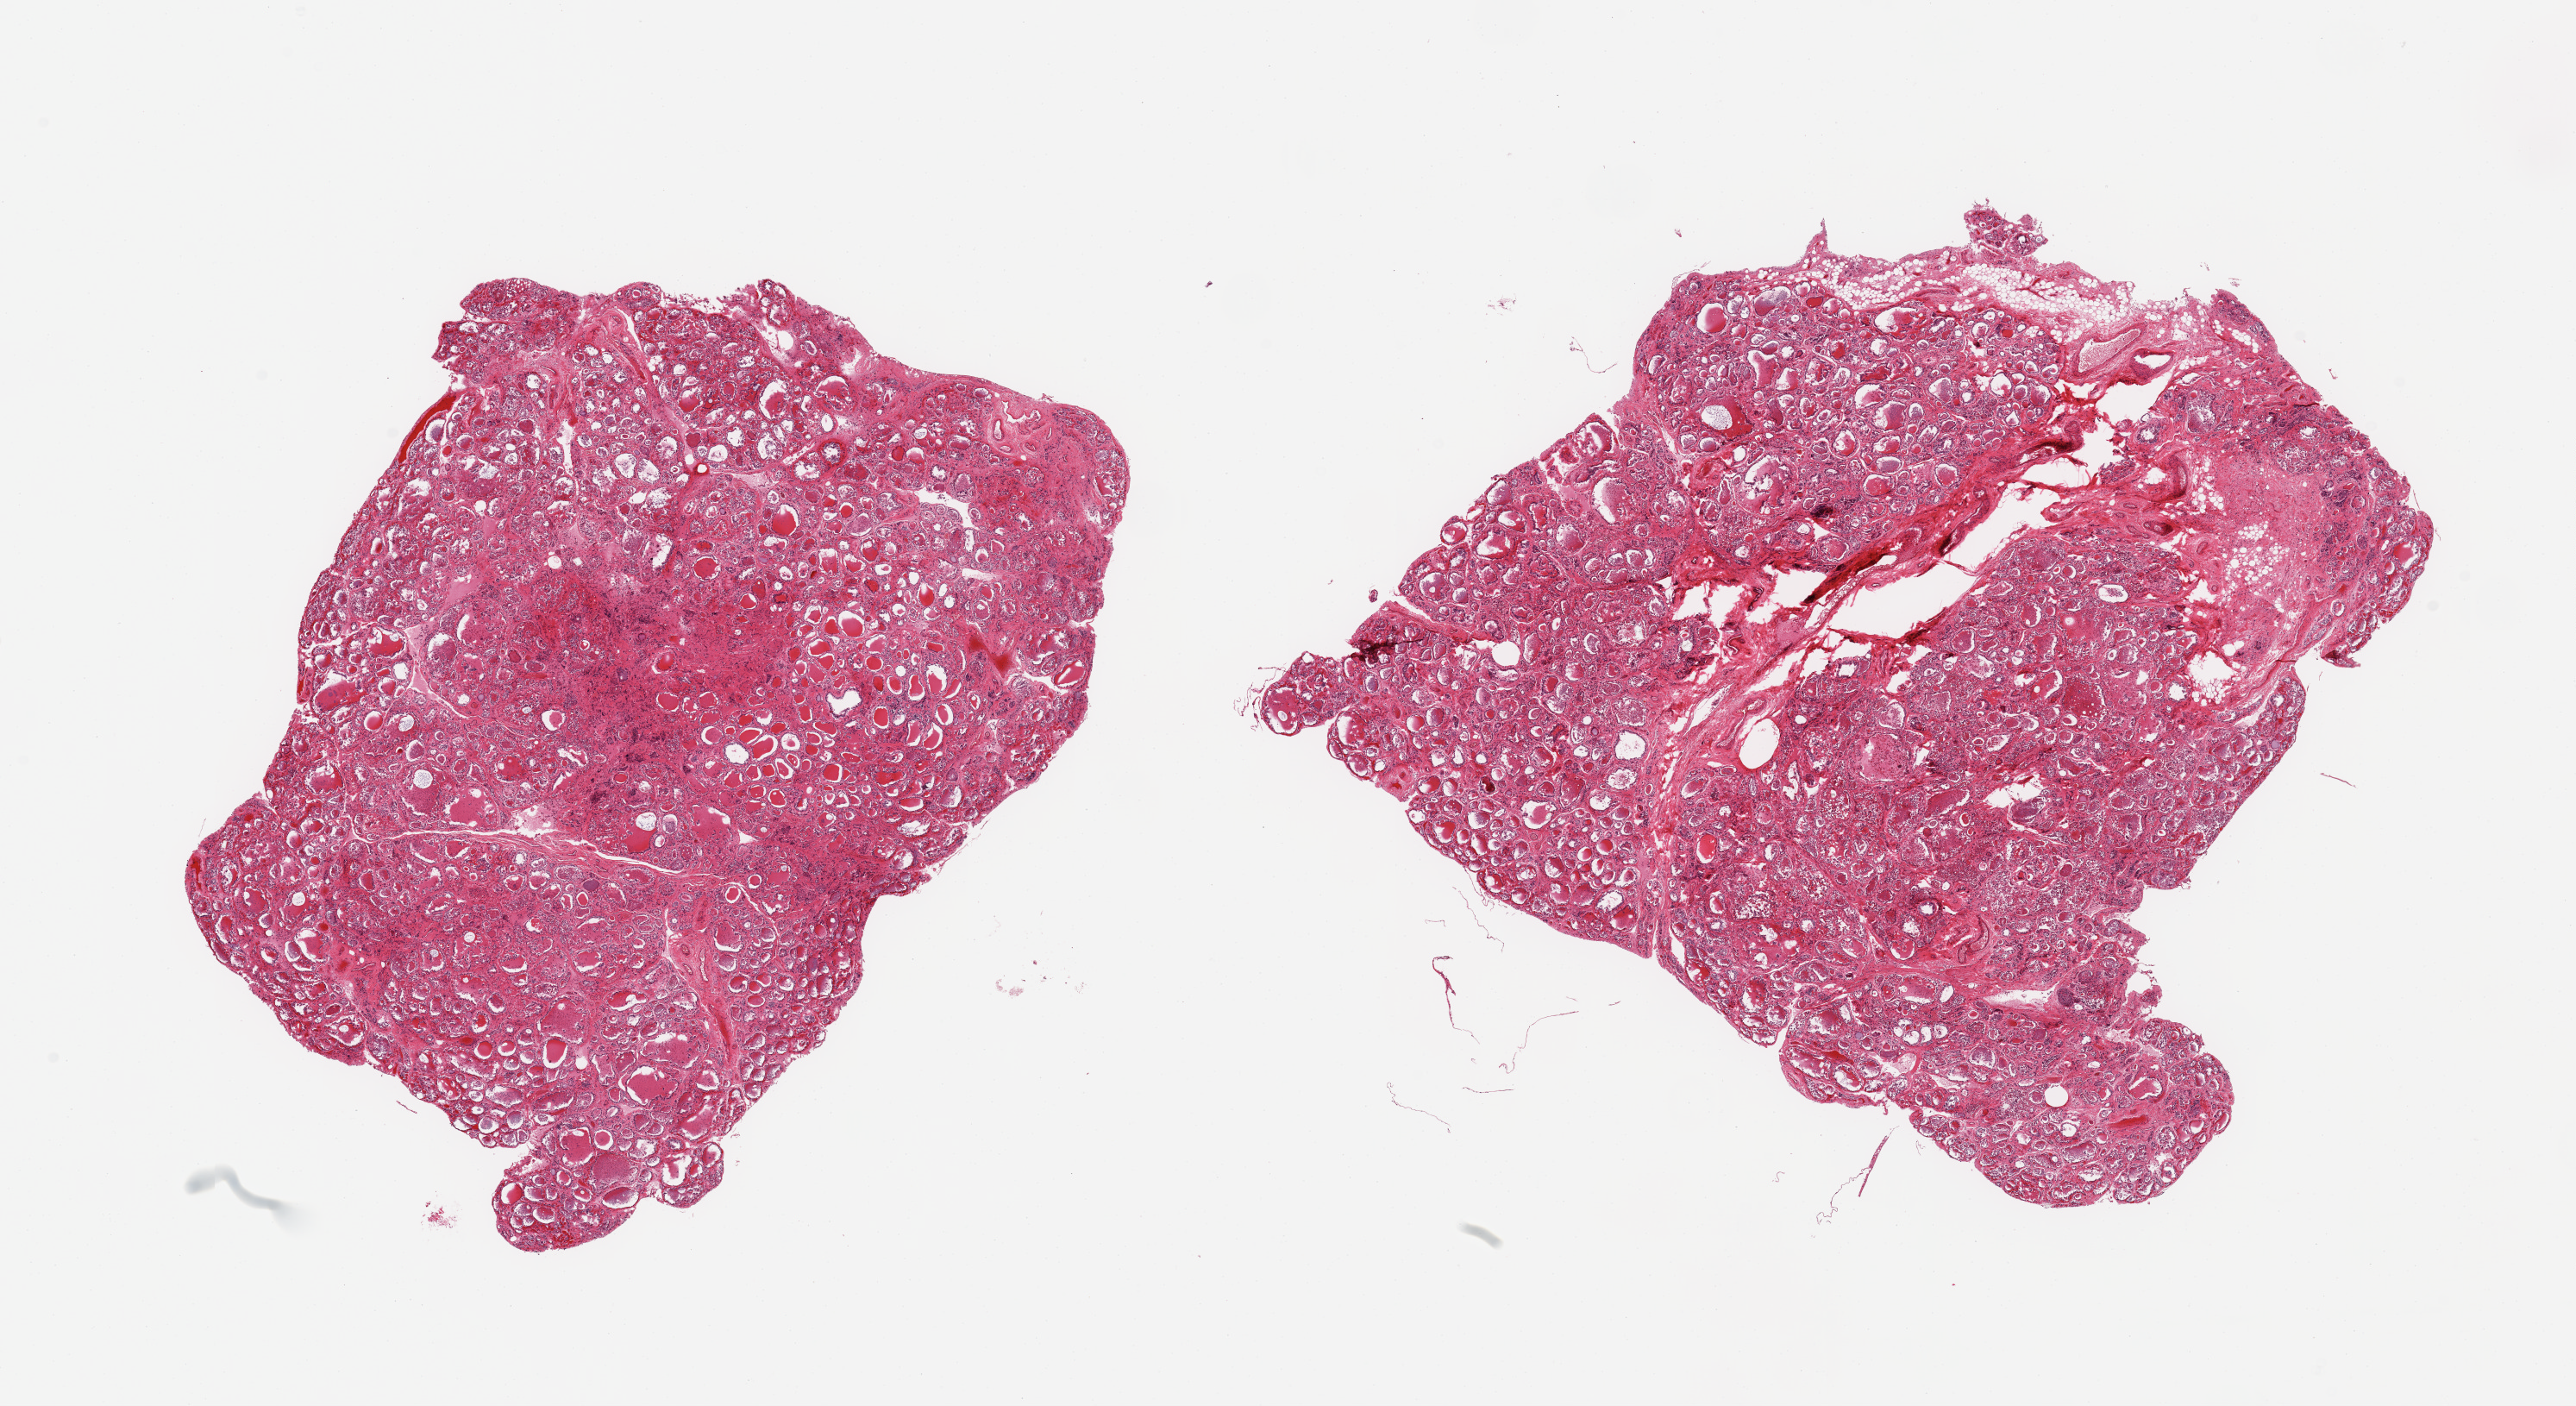
Digitized hematoxylin and eosin (H&E)-stained section, brightfield — low-resolution overview of the scanned area, about 23.6 x 12.9 mm (slide scanned at 20x). PAXgene-fixed paraffin-embedded (PFPE) section. Sampled site (target tissue): thyroid. Tissue donor sample. Male donor.
Review note (as recorded): 2 pieces, goitre with regressive changes.